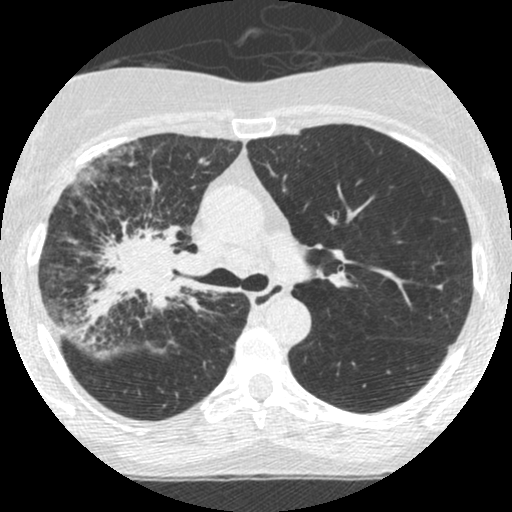
Low-dose screening chest CT, one axial slice; slice 170 of 253 in the series (ordered by position); lung window (W 1500 / L -600 HU); 512 × 512 image matrix, field of view 294 × 294 mm.
Structures marked on this image (outlined manually by an expert reader):
- lesion 2 (tumor, hilum of right lung): bounding box (x1, y1, x2, y2) in pixels: (76, 216, 200, 324)